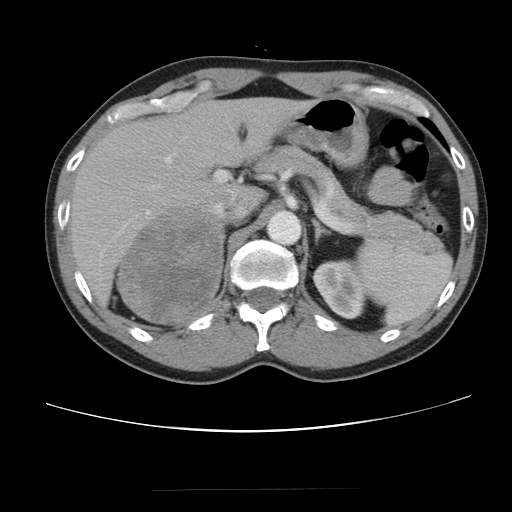
Contrast-enhanced abdominal CT, one axial slice. Position 66 of 80 along the scan axis. Reconstruction kernel STANDARD. Soft-tissue window (W 400 / L 40 HU). 5 mm slice thickness. 512 × 512 image matrix, field of view 360 × 360 mm. Patient: male, 61 years. Case-level facts recorded for this patient, not image findings: diagnosis: adrenocortical carcinoma; tumour side: right adrenal; tumour size at pathology: 11.1 cm; Ki-67 index: 32 %; stage (as recorded): 2.
Structures marked on this image (semi-automatically segmented with operator editing):
- mass: bounding box [x1, y1, x2, y2] px = [119, 207, 223, 323]